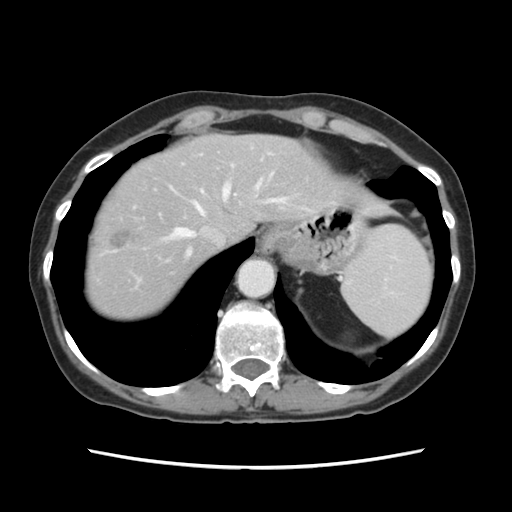
Contrast-enhanced abdominal CT, one axial slice; slice 99 of 120 in the series (ordered by position); 120 kVp; intravenous contrast given; soft-tissue window (W 400 / L 40 HU); 512 × 512 image matrix, field of view 330 × 330 mm. Female patient, age 70 years. From the clinical record (not read from this slice): diagnosis: colorectal cancer liver metastases, imaged before liver resection; multiple liver metastases: no; largest metastasis: 2.5 cm; disease in both lobes: no.
Outlined on this slice (expert manual segmentation):
- hepatic veins: bounding box [x1, y1, x2, y2] px = [173, 181, 286, 258]
- liver: [88, 136, 352, 320]
- planned liver remnant (the part of the liver to remain after resection): [145, 135, 352, 264]
- portal vein (with intrahepatic branches): [201, 153, 272, 196]
- liver metastasis: [111, 230, 131, 248]